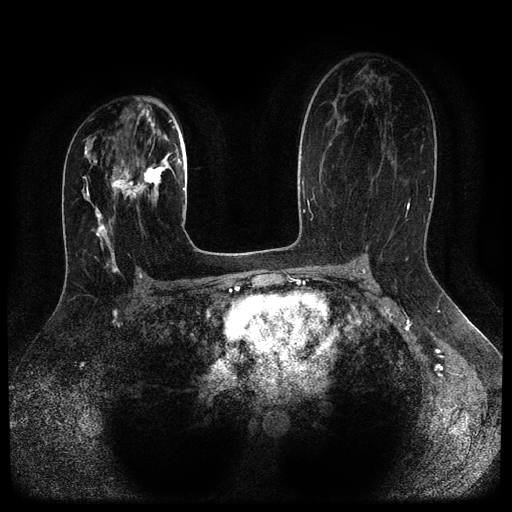
Breast MRI (dynamic contrast-enhanced, multi-phase), one axial slice. Position 61 of 116 along the scan axis. Dynamic contrast-enhanced series, time point 2 of 5 at this slice position (early post-contrast). 1.5 T. TE 2.6 ms, TR 5.4 ms. 2 mm slice thickness. 512 × 512 image matrix, field of view 340 × 340 mm. Patient: female, 29 years.
Annotated regions visible in this slice (semi-automatic segmentation, software-assisted and operator-edited):
- breast lesion (labelled 'tumour' in the annotation; benign lesions carry a separate 'benign' label): bounding box [x1, y1, x2, y2] px = [111, 157, 172, 206]
- breast lesion (labelled benign in the annotation): [93, 207, 118, 273]